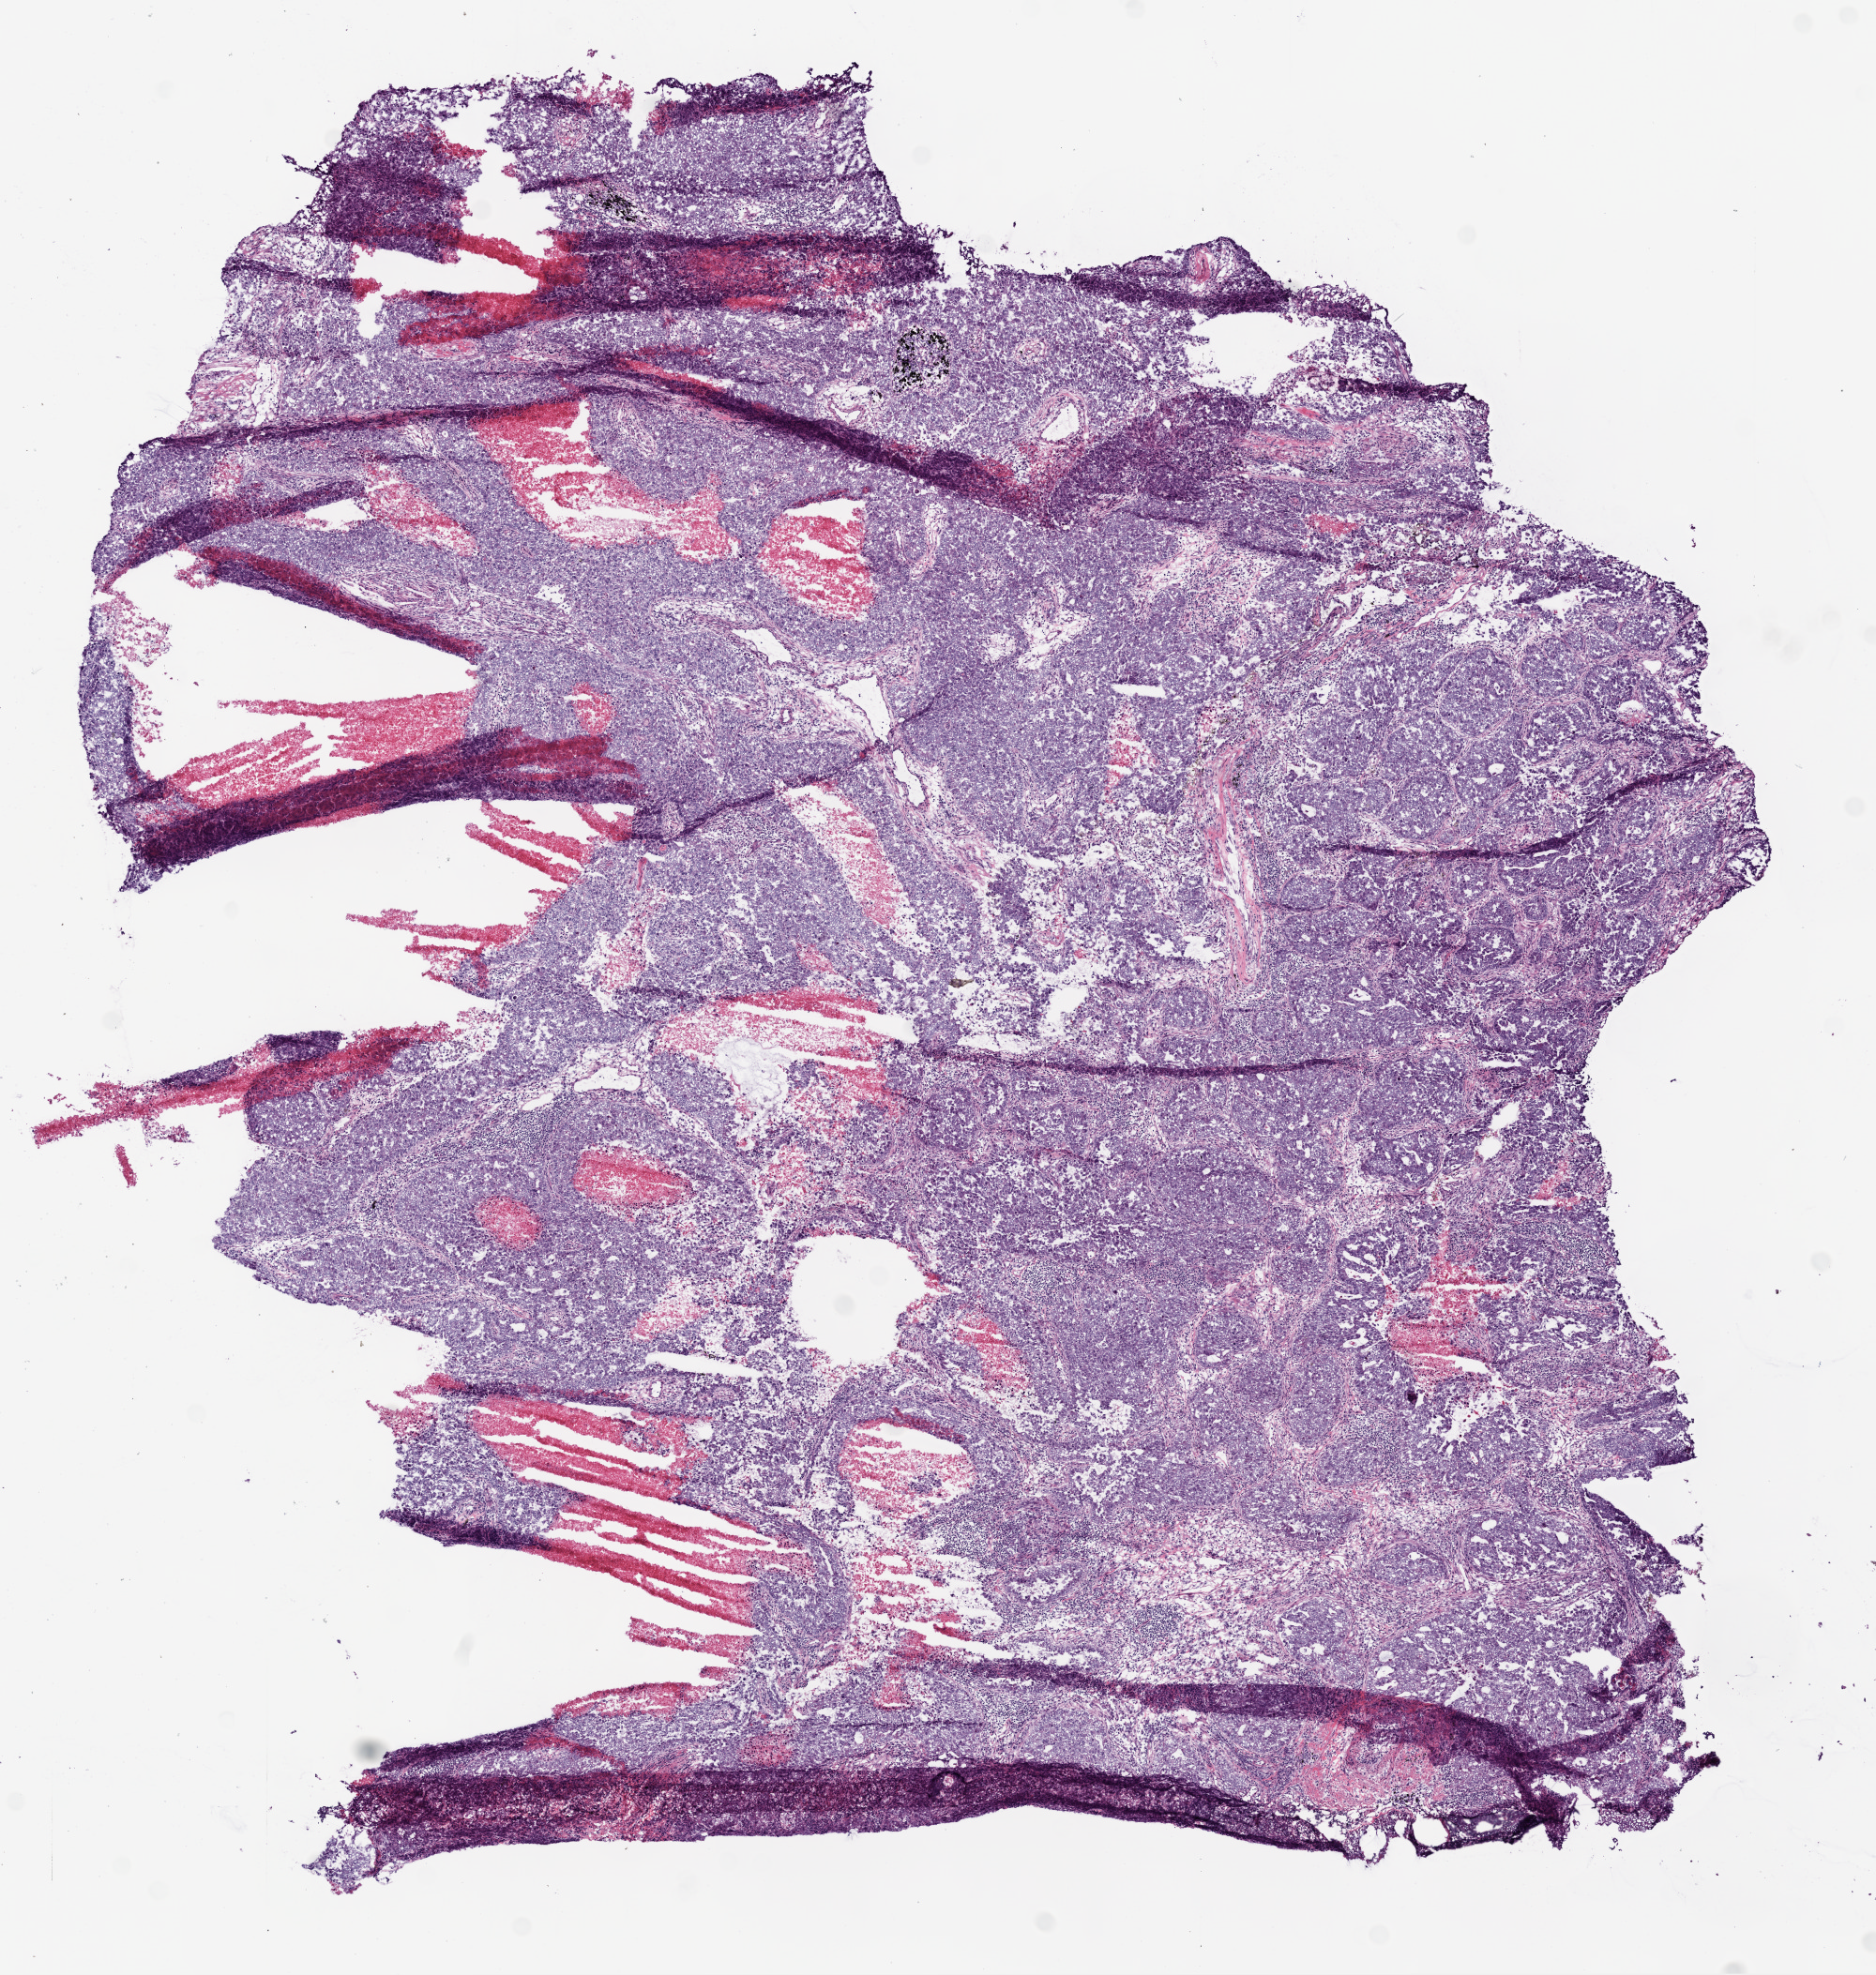
Digitized Hematoxylin and eosin (H&E) stained tissue section (whole slide) — shown as a low-resolution overview of the whole scanned area (about 8.0 x 8.4 mm, acquisition: 20x scan), frozen section, lung, primary tumour sample. Male patient; age at initial diagnosis 55 years. Pathologist review of this section (percent, as recorded): tumour cells 85%, tumour nuclei 85%, normal cells 0%, stromal cells 5%, necrosis 10%. Infiltration values recorded for this section: lymphocyte infiltration 4%.
* histologic diagnosis: Adenocarcinoma, NOS (upper lobe, lung)
* laterality: right
* AJCC pathologic stage: IIB (6th edition)